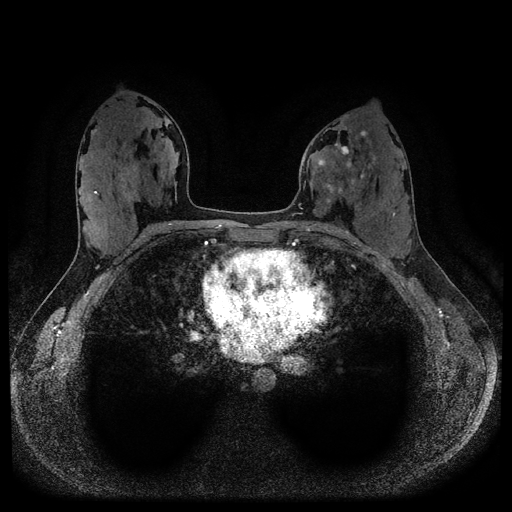
Breast MRI (dynamic contrast-enhanced, multi-phase), one axial slice; position 52 of 116 along the scan axis; dynamic contrast-enhanced series, time point 2 of 5 at this slice position (early post-contrast); 1.5 T; TE 2.6 ms, TR 5.3 ms; 2 mm slice thickness; 512 × 512 image matrix, field of view 350 × 350 mm. Patient: female, 33 years.
Structures marked on this image (semi-automatic segmentation, software-assisted and operator-edited):
- breast lesion (labelled 'tumour' in the annotation; benign lesions carry a separate 'benign' label): bounding box [x1, y1, x2, y2] px = [317, 145, 356, 198]